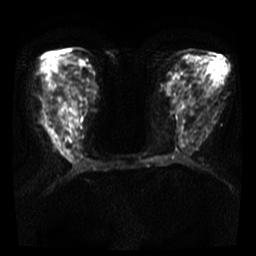
Breast MRI, one axial slice. Position 17 of 36 along the scan axis. Diffusion-weighted series; image 2 of 4 stored at this slice position (different b-values; order by instance number). 3 T. 5 mm slice thickness. 256 × 256 image matrix. Female patient.
Annotated regions visible in this slice (outlined manually by an expert reader):
- tumour on diffusion-weighted imaging: bounding box [x1, y1, x2, y2] px = [57, 143, 64, 155]